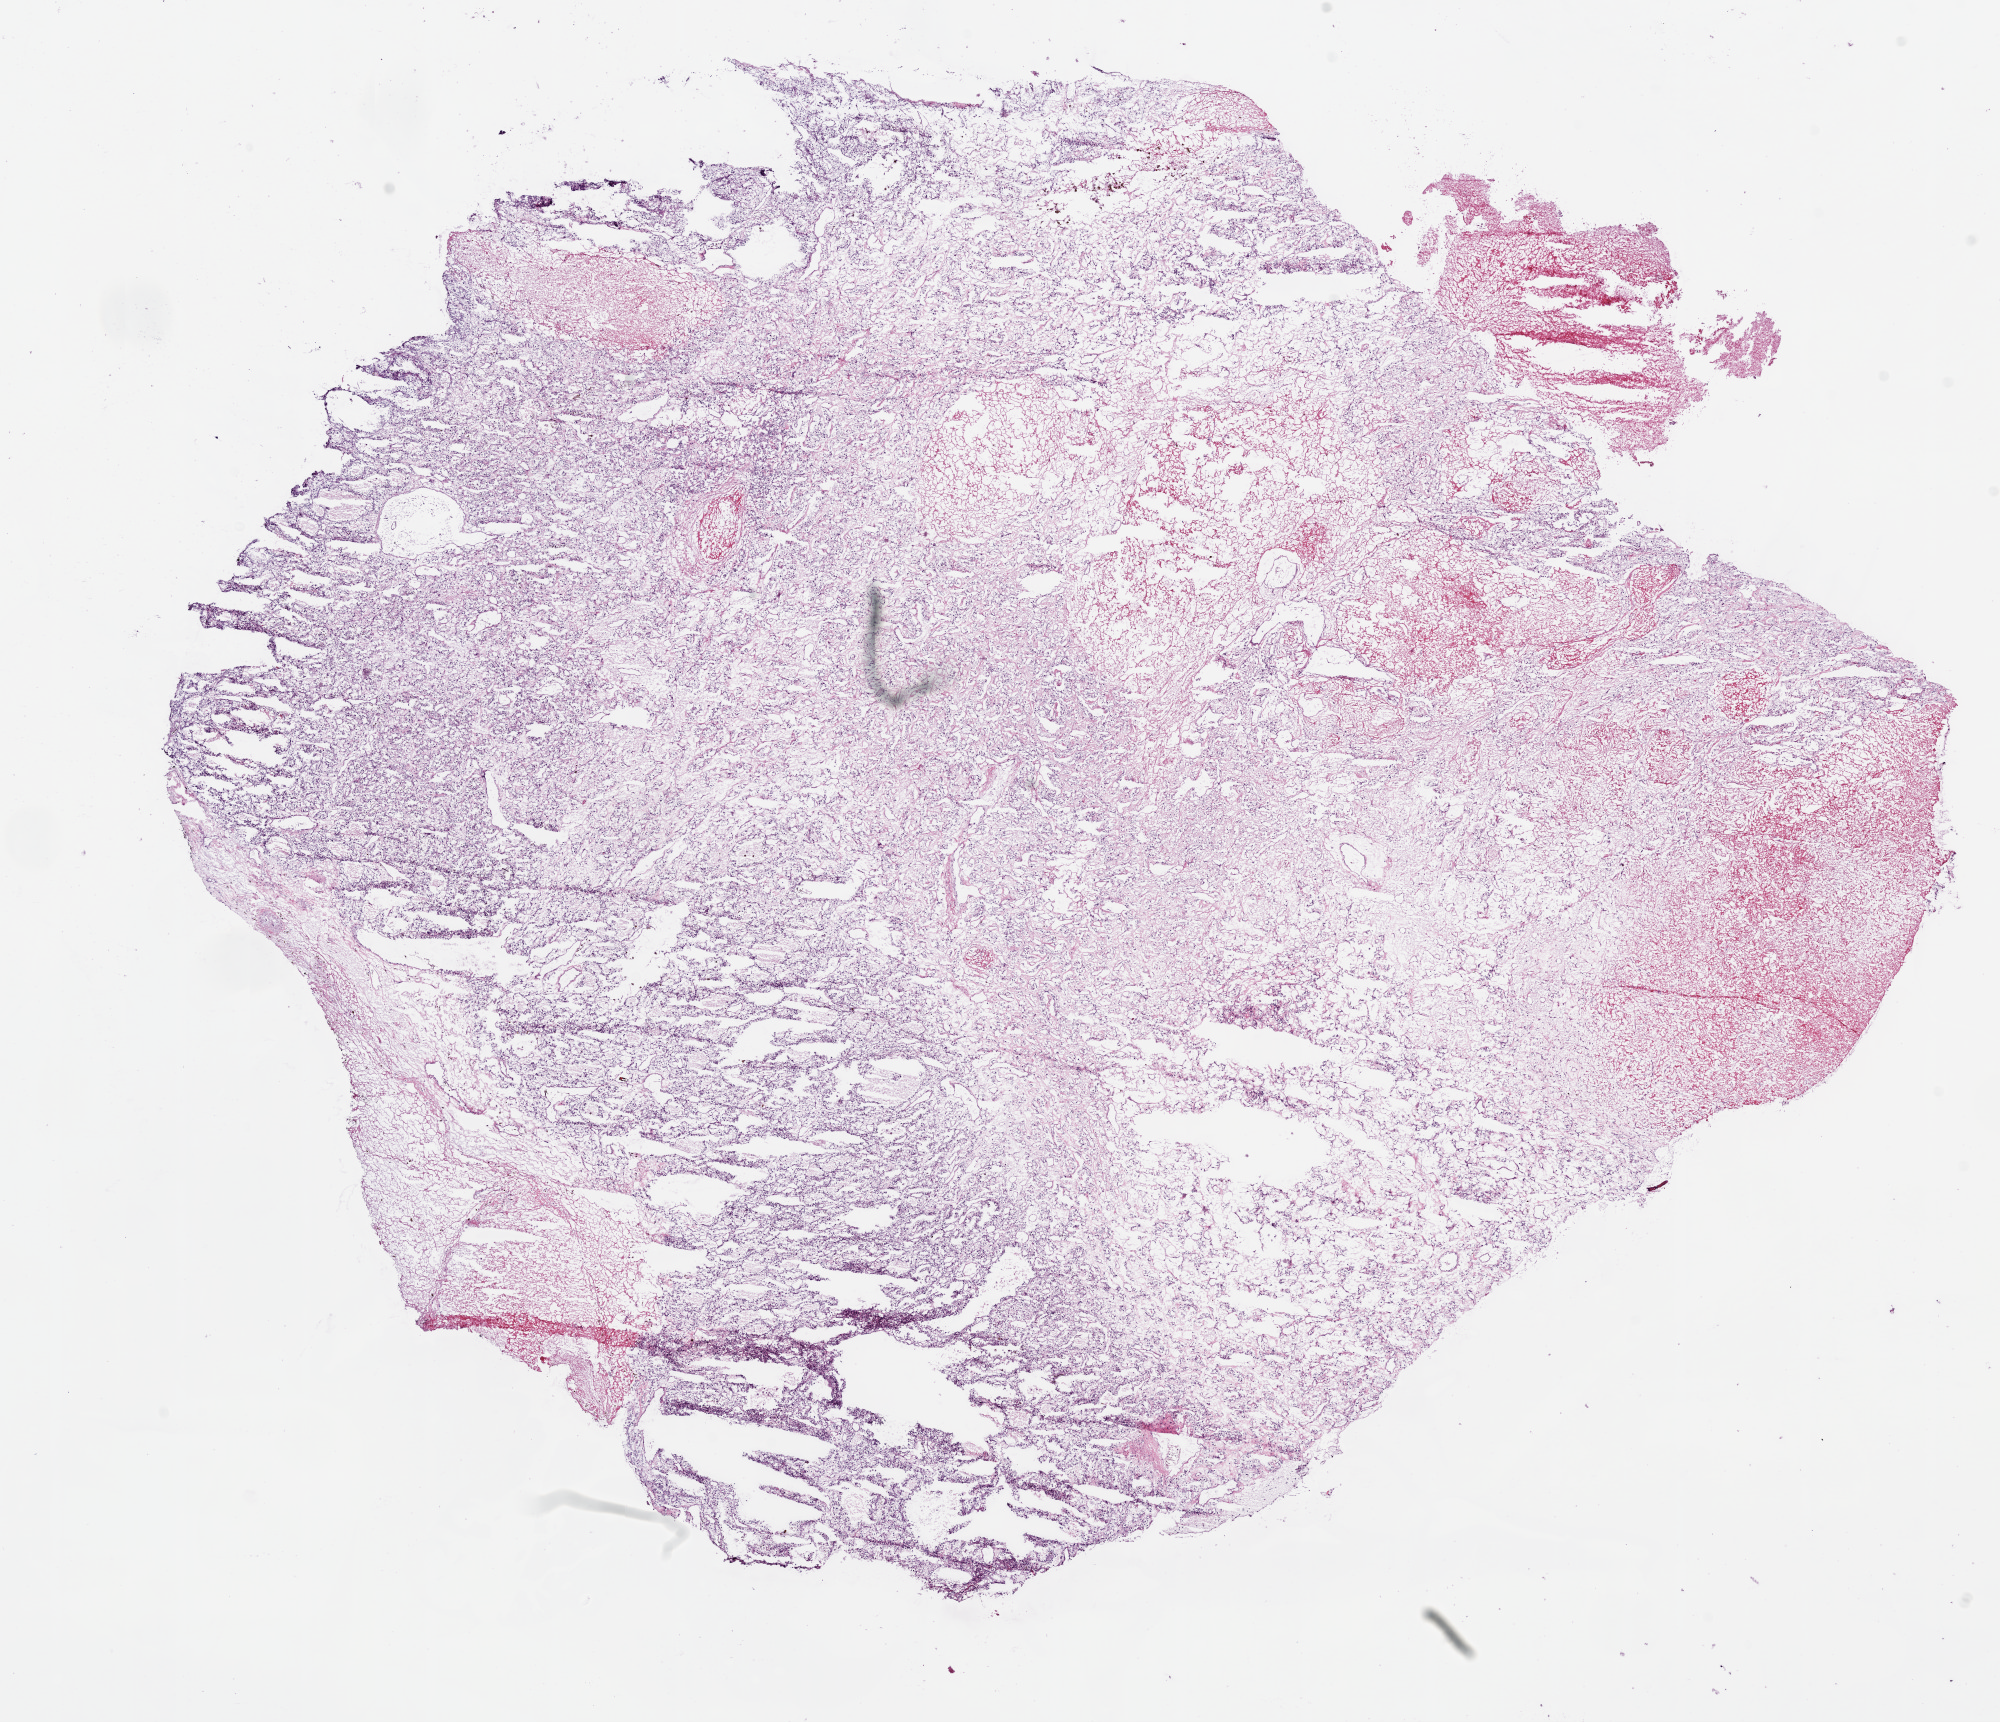
Whole-slide histology image, H&E — whole scanned area (about 16.0 x 13.8 mm, from a 20x scan) shown as a low-resolution overview; frozen section from the bottom of the tissue portion; kidney, primary tumour sample. Male, age 61 years at initial diagnosis. Histologic grade: G2 (moderately differentiated). Slide review estimates, as recorded: tumour cells 73%, tumour nuclei 80%, normal cells 0%, stromal cells 25%, necrosis 2%.
- pathologic diagnosis: Clear cell adenocarcinoma, NOS
- laterality: left
- AJCC pathologic stage: I